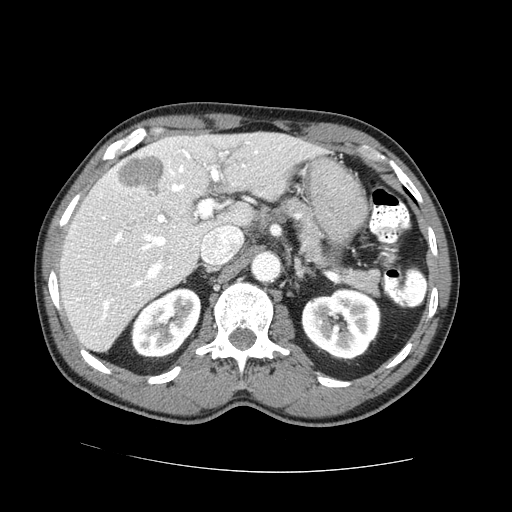
Contrast-enhanced abdominal CT (liver protocol), one axial slice; slice 44 of 73 in the series (ordered by position); 100 kVp; one of 2 acquisitions stored at this slice position; soft-tissue window (W 400 / L 40 HU); 512 × 512 image matrix. Case-level facts recorded for this patient, not image findings: diagnosis: hepatocellular carcinoma (patient treated with transarterial chemoembolisation; whether this scan precedes or follows treatment is not stated here); TNM stage (as recorded): Stage-IVA; Child-Pugh class: A.
Annotated regions visible in this slice (semi-automatically segmented with operator editing):
- liver parenchyma outside the tumour (the mass and vessels are separate outlines, so this box may not span the whole liver): bounding box [x1, y1, x2, y2] px = [58, 132, 322, 352]
- mass: [119, 155, 163, 193]
- liver vessels: [70, 142, 258, 320]